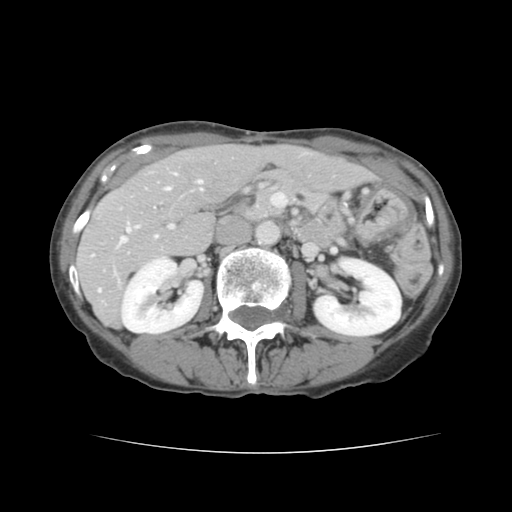
Contrast-enhanced abdominal CT, one axial slice. Position 65 of 136 along the scan axis. 120 kVp. Soft-tissue window (W 400 / L 40 HU). 2.5 mm slice thickness. 512 × 512 image matrix, field of view 319 × 319 mm. Female patient, age 77 years. From the clinical record (not read from this slice): diagnosis: colorectal cancer liver metastases, imaged before liver resection; multiple liver metastases: yes; largest metastasis: 3 cm; chemotherapy before resection: yes.
Outlined on this slice (outlined manually by an expert reader):
- hepatic veins: bounding box [x1, y1, x2, y2] px = [121, 173, 202, 243]
- liver: [78, 145, 372, 325]
- planned liver remnant (the part of the liver to remain after resection): [161, 145, 372, 206]
- portal vein (with intrahepatic branches): [98, 224, 173, 292]